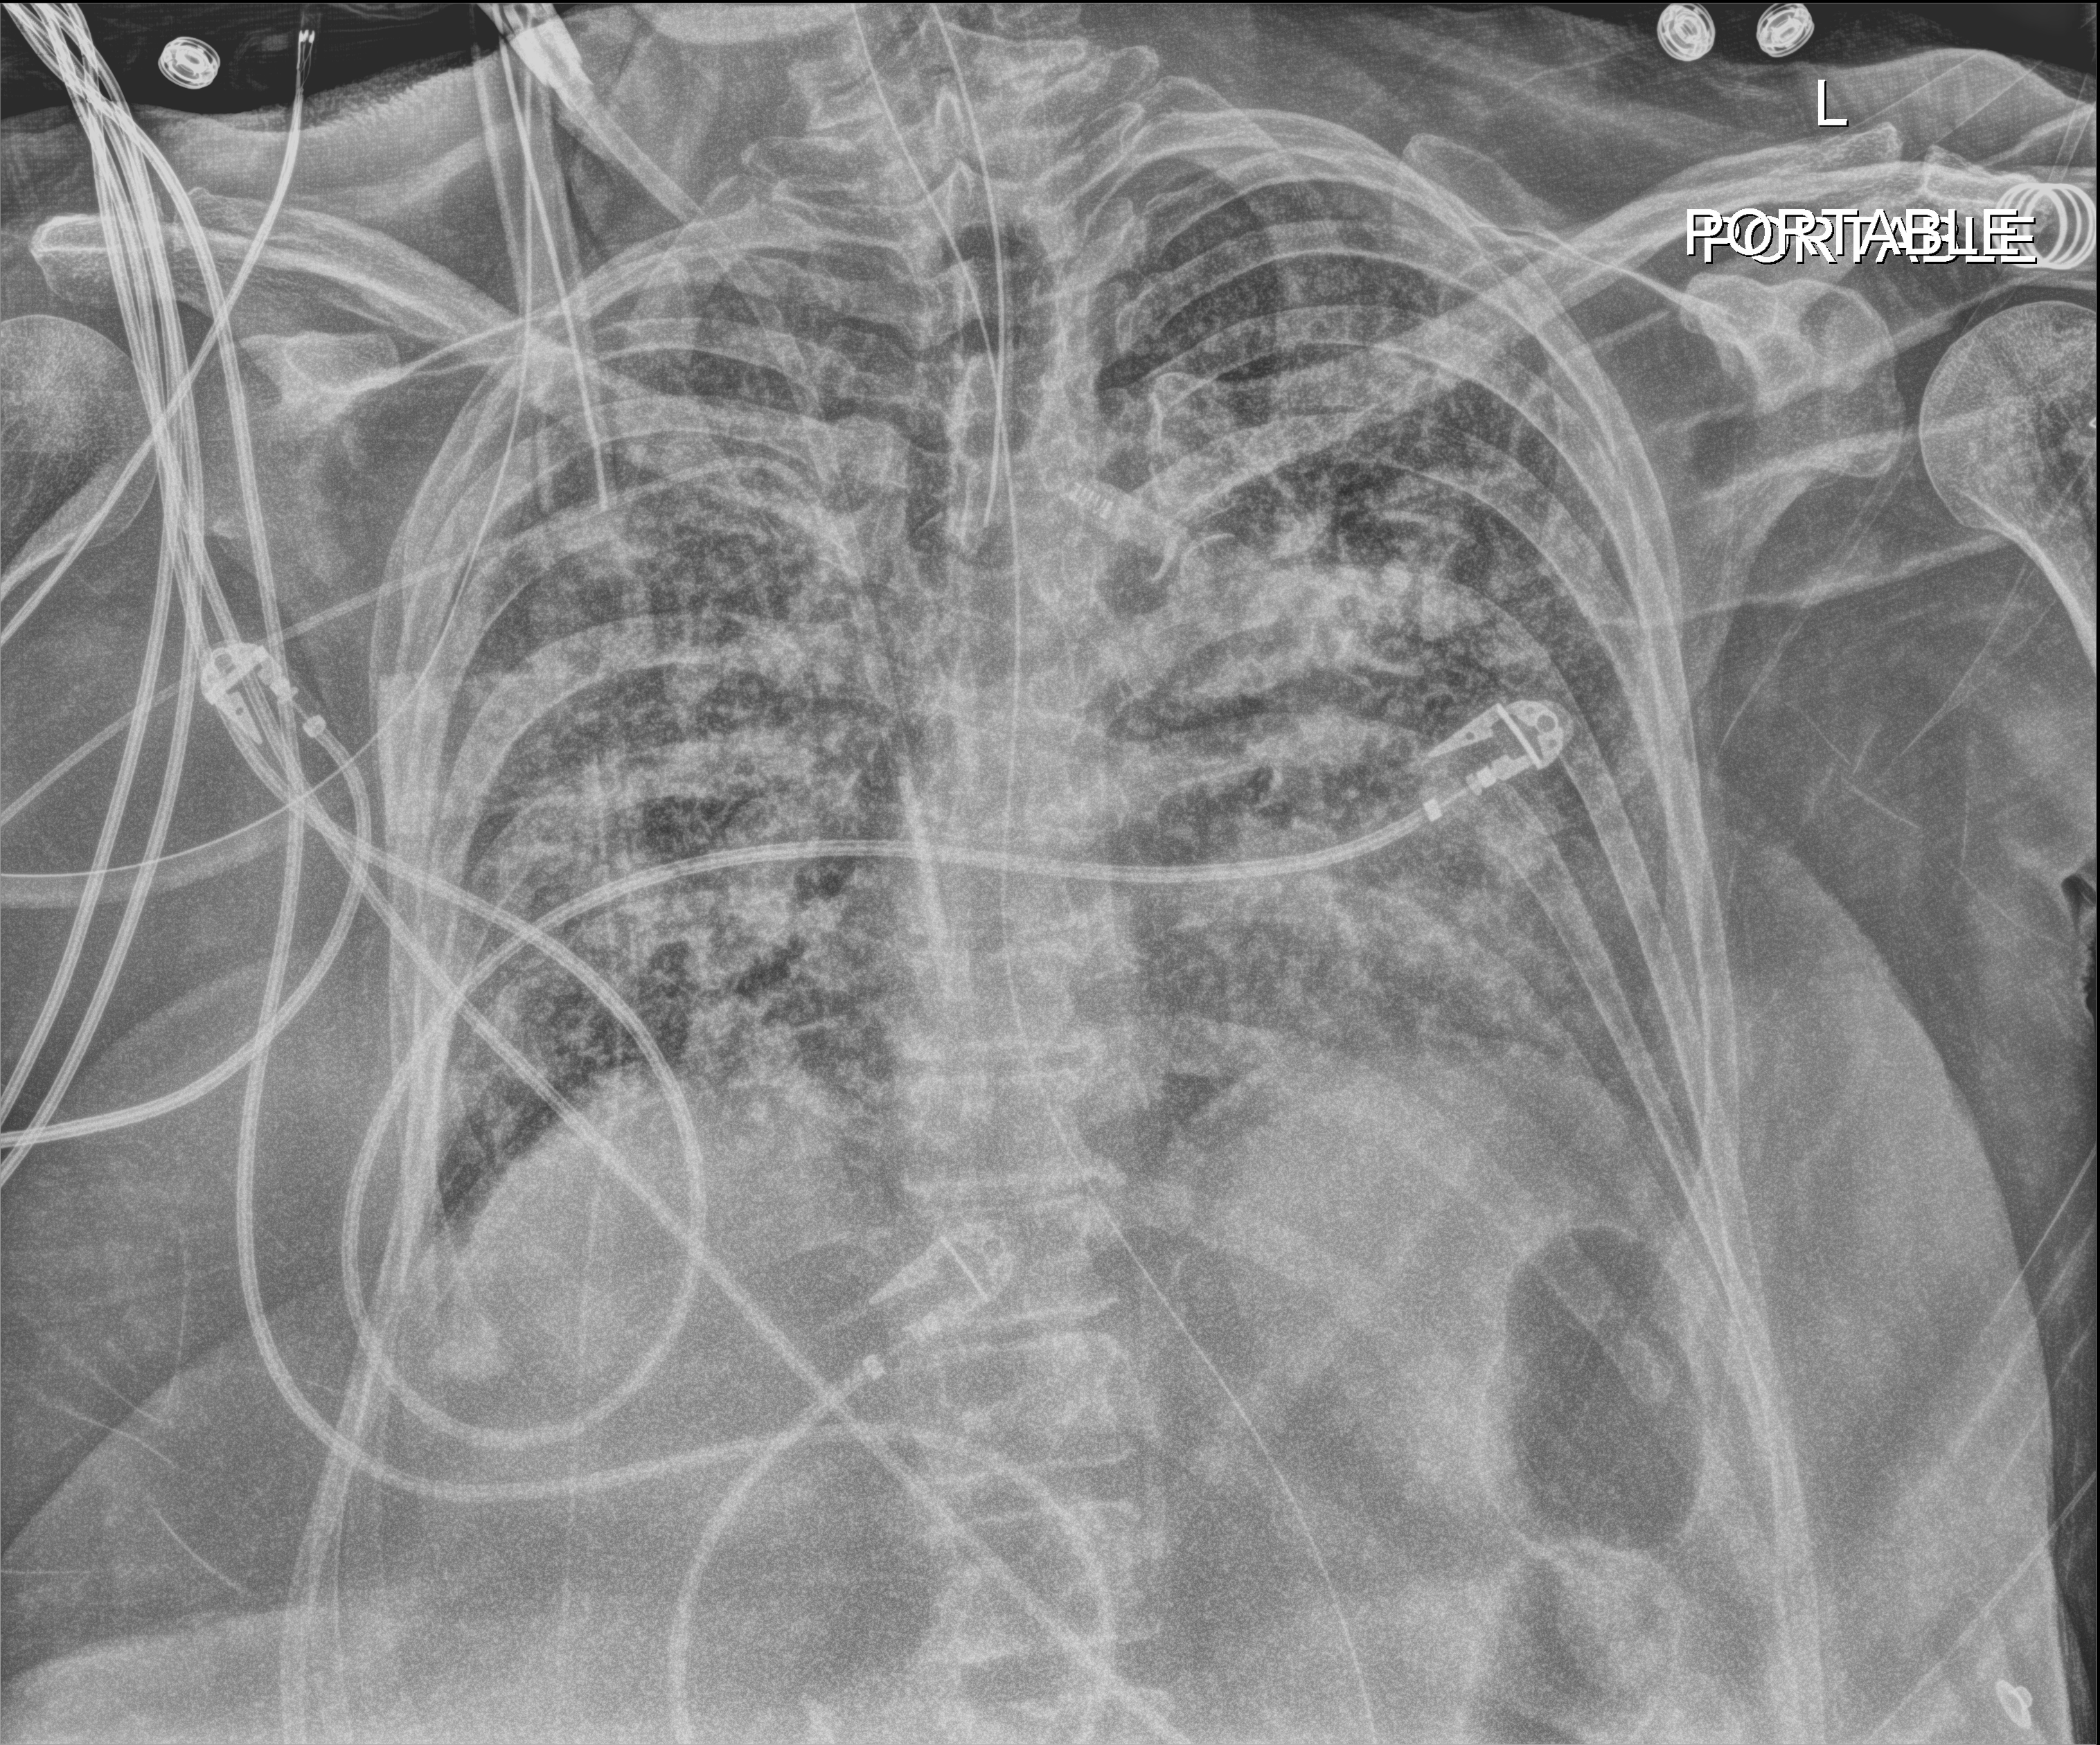
Portable chest radiograph, anteroposterior (AP) projection. Patient hospitalised with COVID-19; female, aged 60–74 years.
Admission-level facts for this patient (not findings on this image; timing relative to this image not recorded):
- admitted to intensive care during this hospital stay: yes
- chronic kidney disease (admission record): no
- length of hospital stay: 45 days